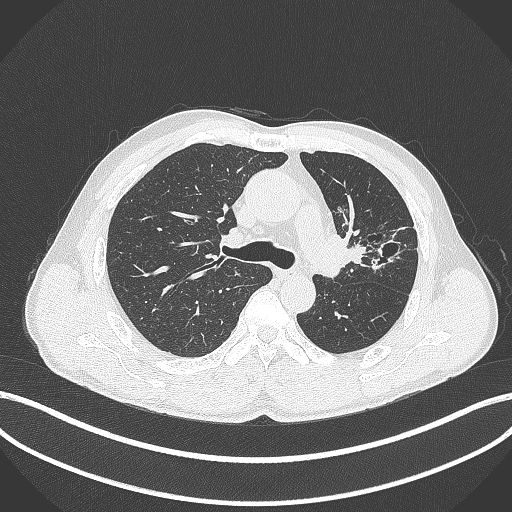
Chest CT, one axial slice; position 273 of 429 along the scan axis; reconstruction kernel B70f; lung window (W 1500 / L -600 HU); 1 mm slice thickness; 512 × 512 image matrix, field of view 400 × 400 mm. Male patient, age 57 years. Case-level facts recorded for this patient, not image findings: clinical TNM (as recorded): T2b N0 M0.
Annotated regions visible in this slice (rectangle marked by the reading radiologist):
- lung tumour (recorded histology: squamous cell carcinoma): bounding box [x1, y1, x2, y2] px = [326, 232, 370, 268]